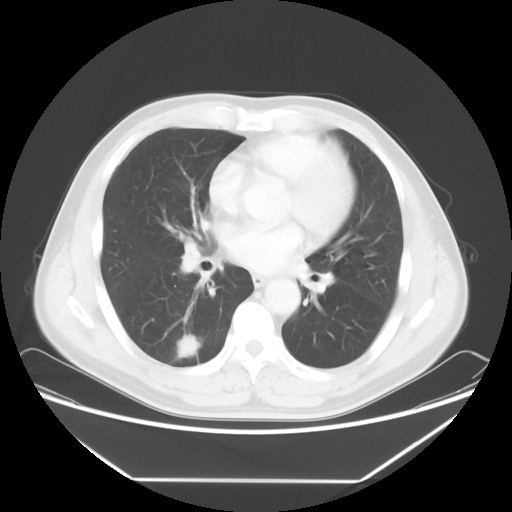
Chest CT, one axial slice. Position 32 of 65 along the scan axis. Lung window (W 1500 / L -600 HU). 5 mm slice thickness. 512 × 512 image matrix, field of view 418 × 418 mm. Male patient, age 50 years. Case-level facts recorded for this patient, not image findings: clinical TNM (as recorded): T1c N0 M0.
Structures marked on this image (rectangle marked by the reading radiologist):
- lung tumour (recorded histology: adenocarcinoma): bounding box (x1, y1, x2, y2) in pixels: (173, 330, 208, 364)